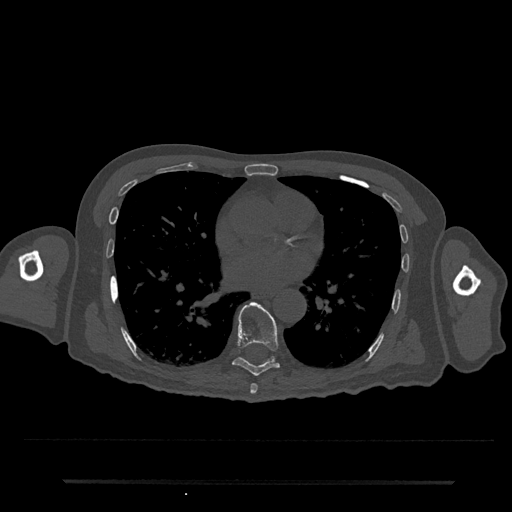
CT including the spine, one axial slice; slice 418 of 797 in the series (ordered by position); 120 kVp; bone window (W 1800 / L 400 HU); 0.5 mm slice thickness; 512 × 512 image matrix. Male patient, age 74 years. Case-level facts recorded for this patient, not image findings: primary cancer: prostate.
Structures marked on this image (semi-automatically segmented with operator editing):
- T7 vertebra: box from (x=250, y=384) to (x=258, y=394) px
- T8 vertebra: (x=232, y=302)–(x=280, y=376)